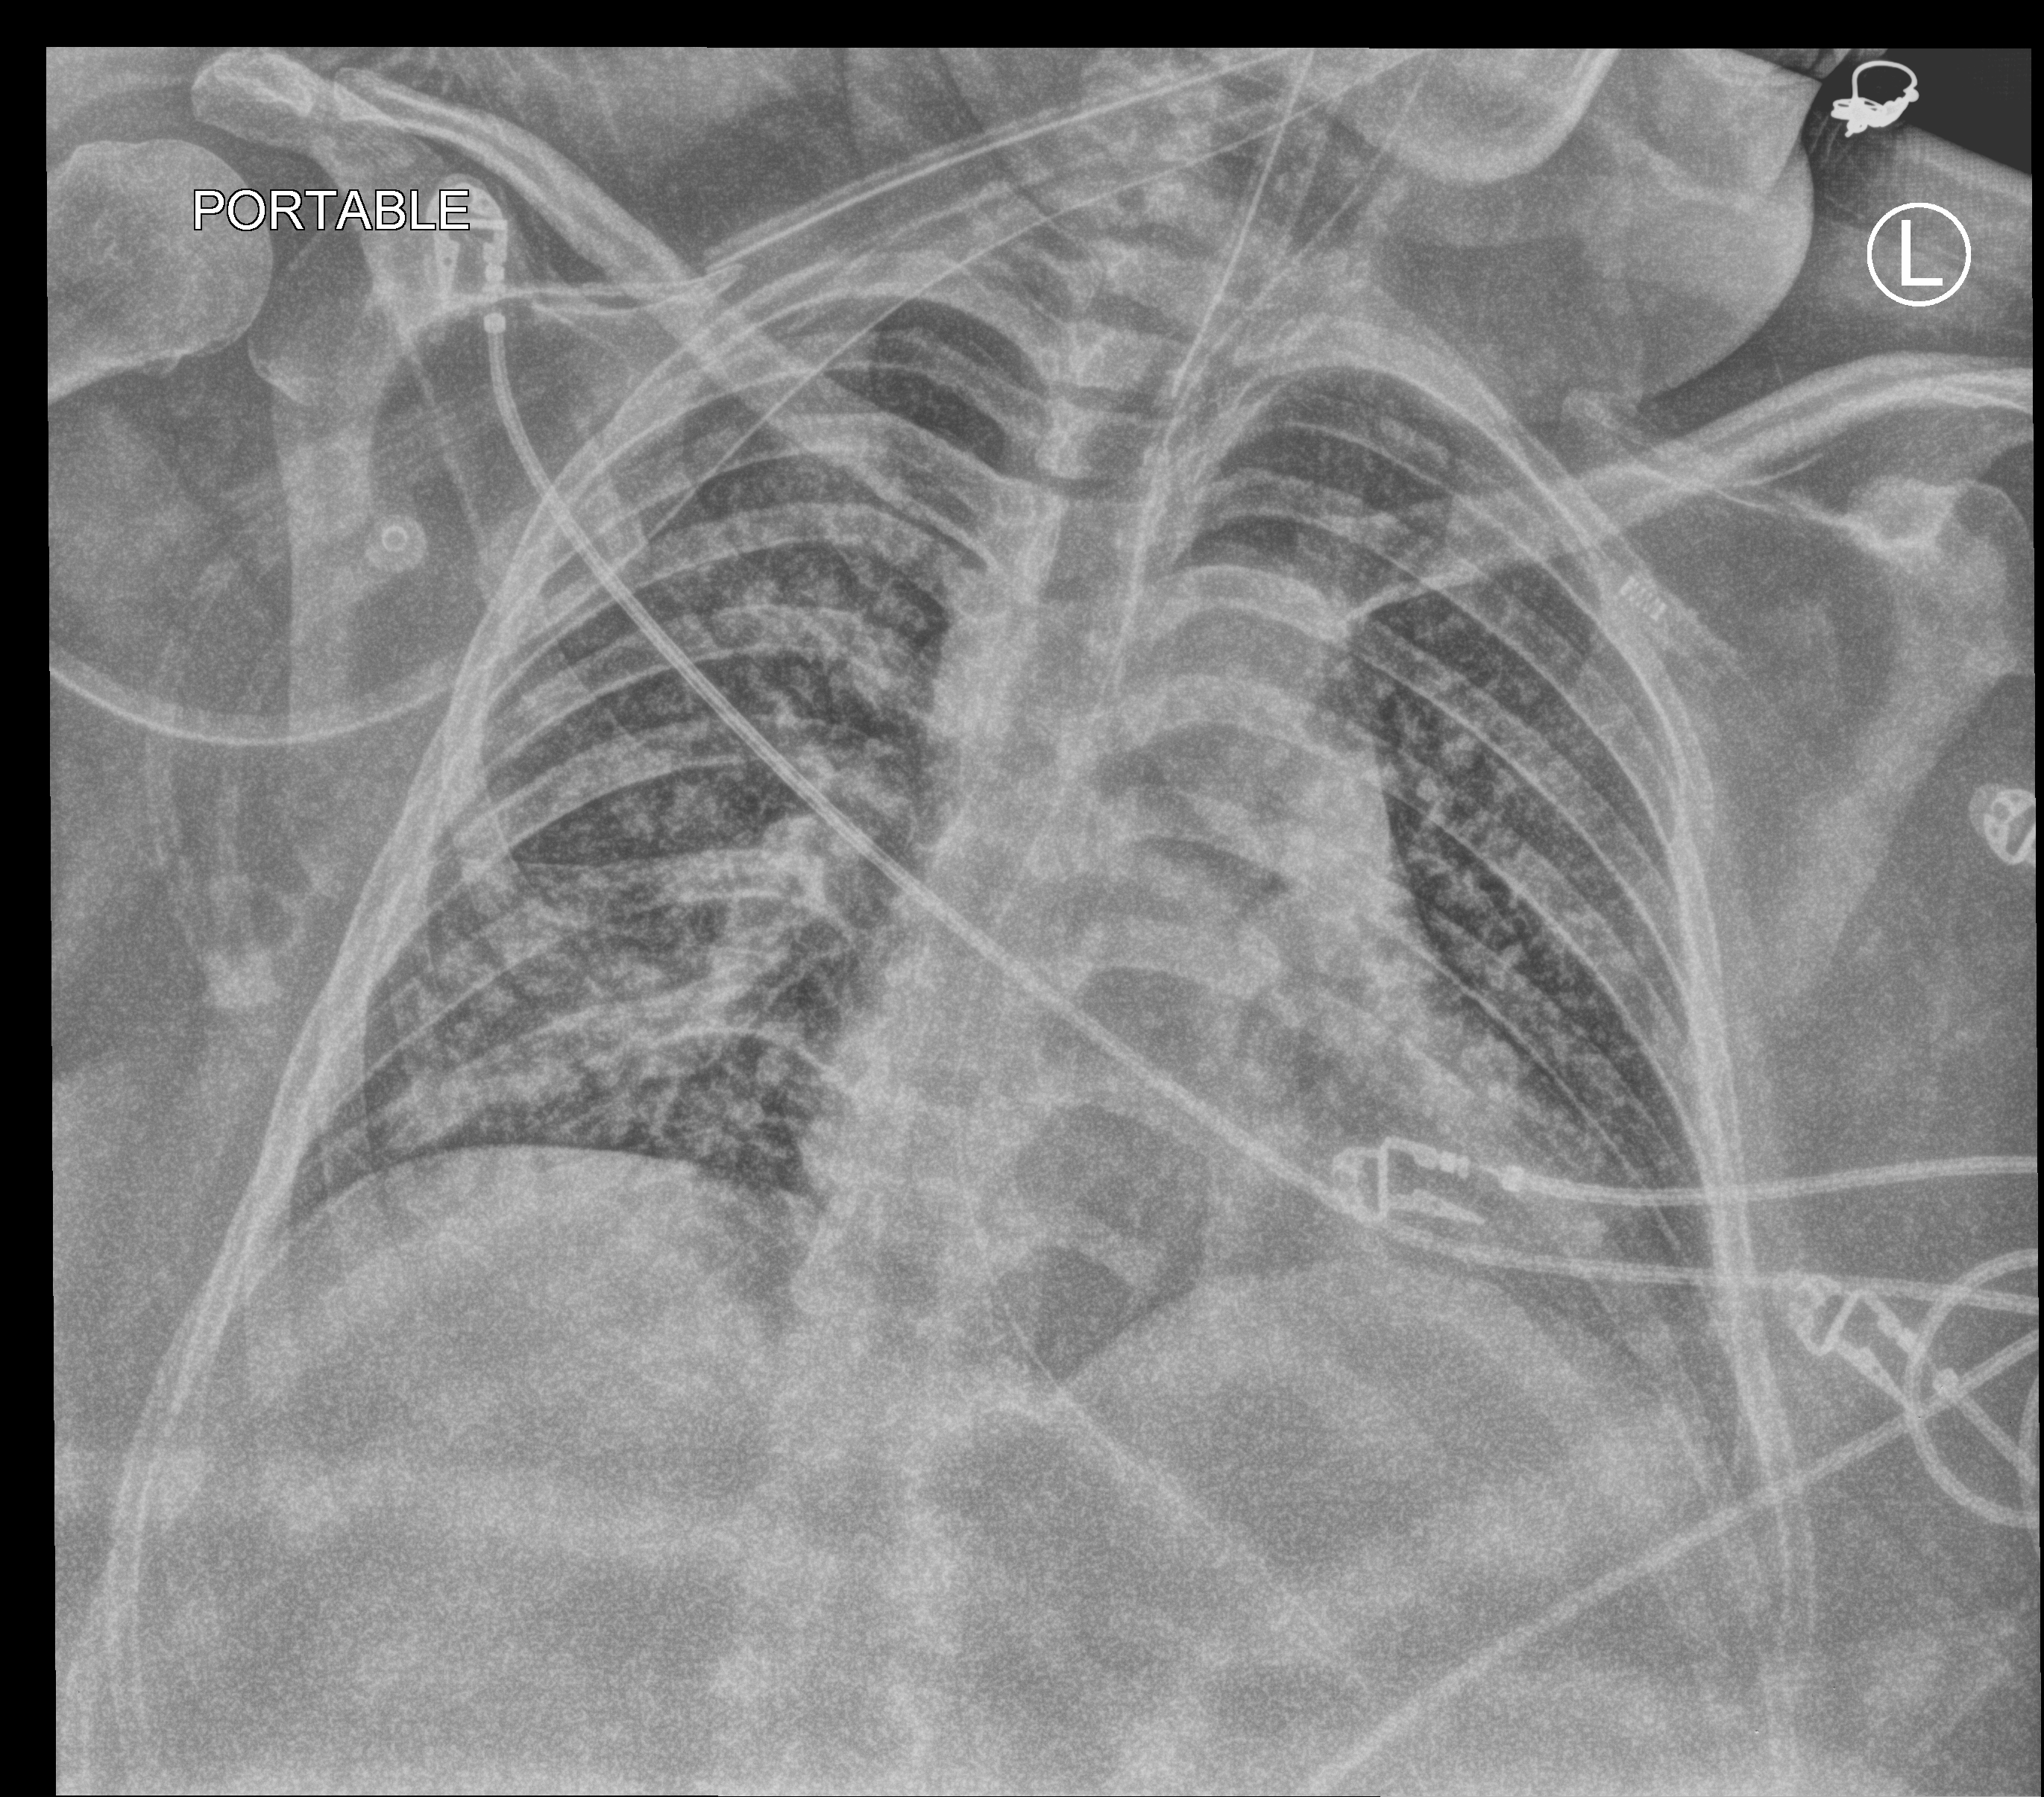
Bedside chest radiograph (computed radiography); anteroposterior (AP) projection. Female patient hospitalised with COVID-19, age 18–59 years.
Hospital-stay facts (about this admission, not read from this image; timing relative to this image not recorded):
- hypertension (admission record): no
- admitted to intensive care during this hospital stay: yes